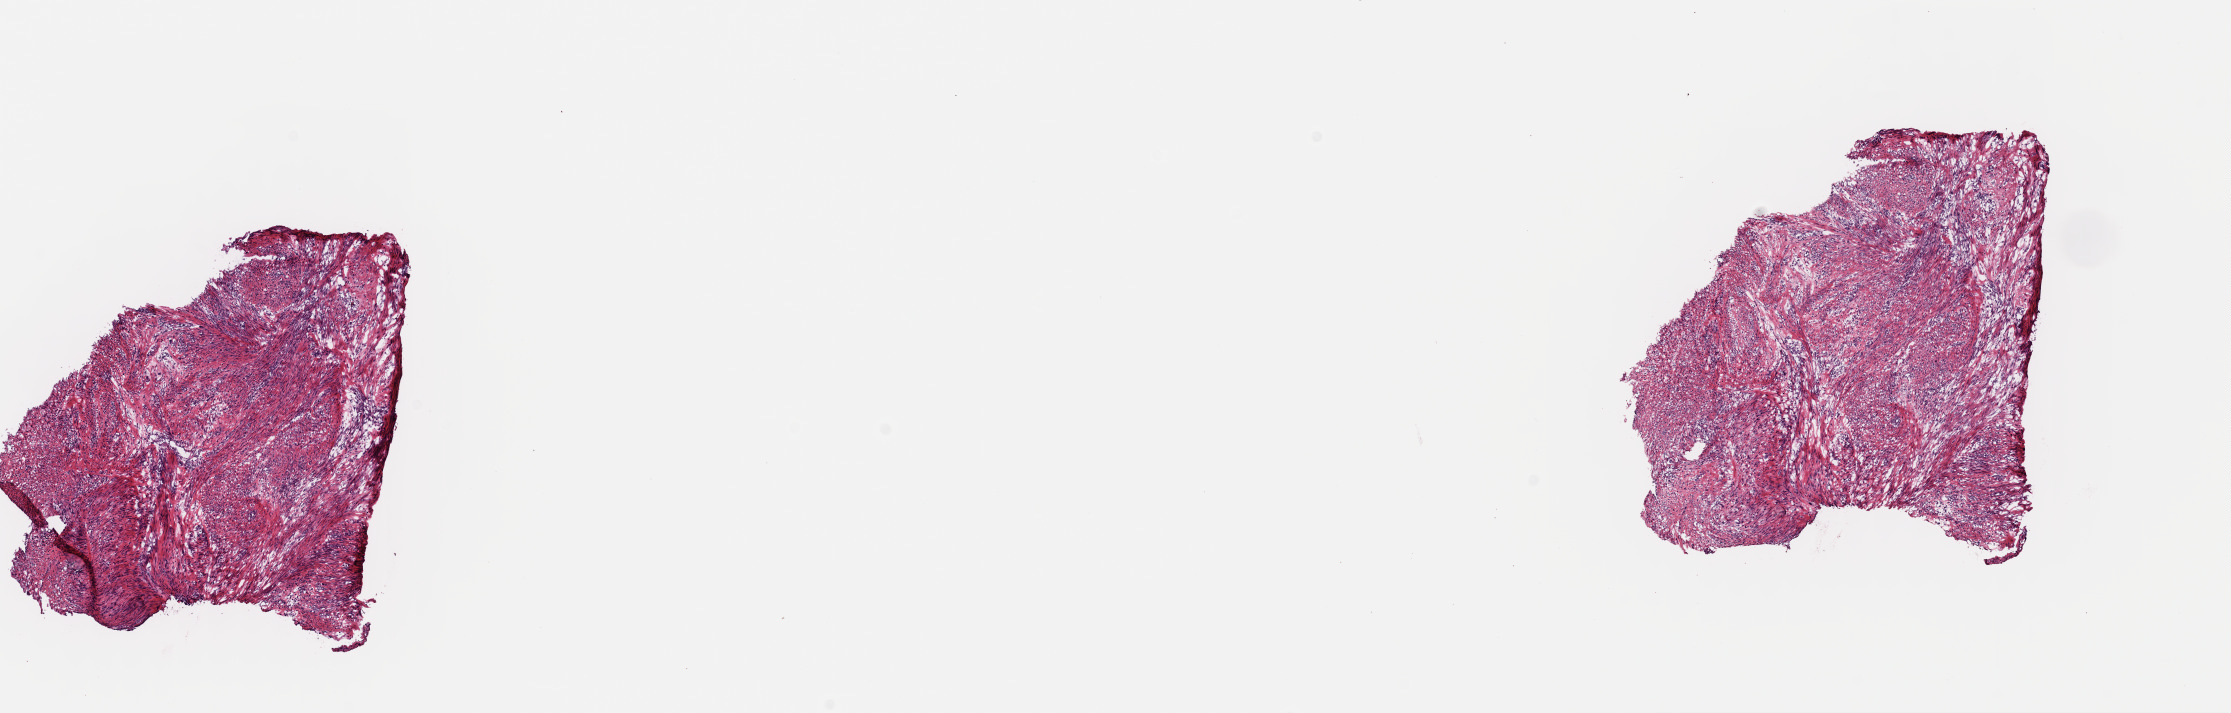
Digitized Hematoxylin and eosin (H&E) stained tissue section (whole slide), shown as a low-resolution overview of the whole scanned area (about 17.6 x 5.6 mm). Frozen section from the top of the tissue portion. Primary tumour sample from the other and unspecified male genital organs. Male patient; age at initial diagnosis 51 years. Composition of this section per pathologist review: tumour cells 90%, tumour nuclei 90%, normal cells 0%, stromal cells 10%, necrosis 0%. Infiltration values recorded for this section: lymphocyte infiltration 0%, monocyte infiltration 0%, neutrophil infiltration 0%.
Pathologic diagnosis: Dedifferentiated liposarcoma (spermatic cord).